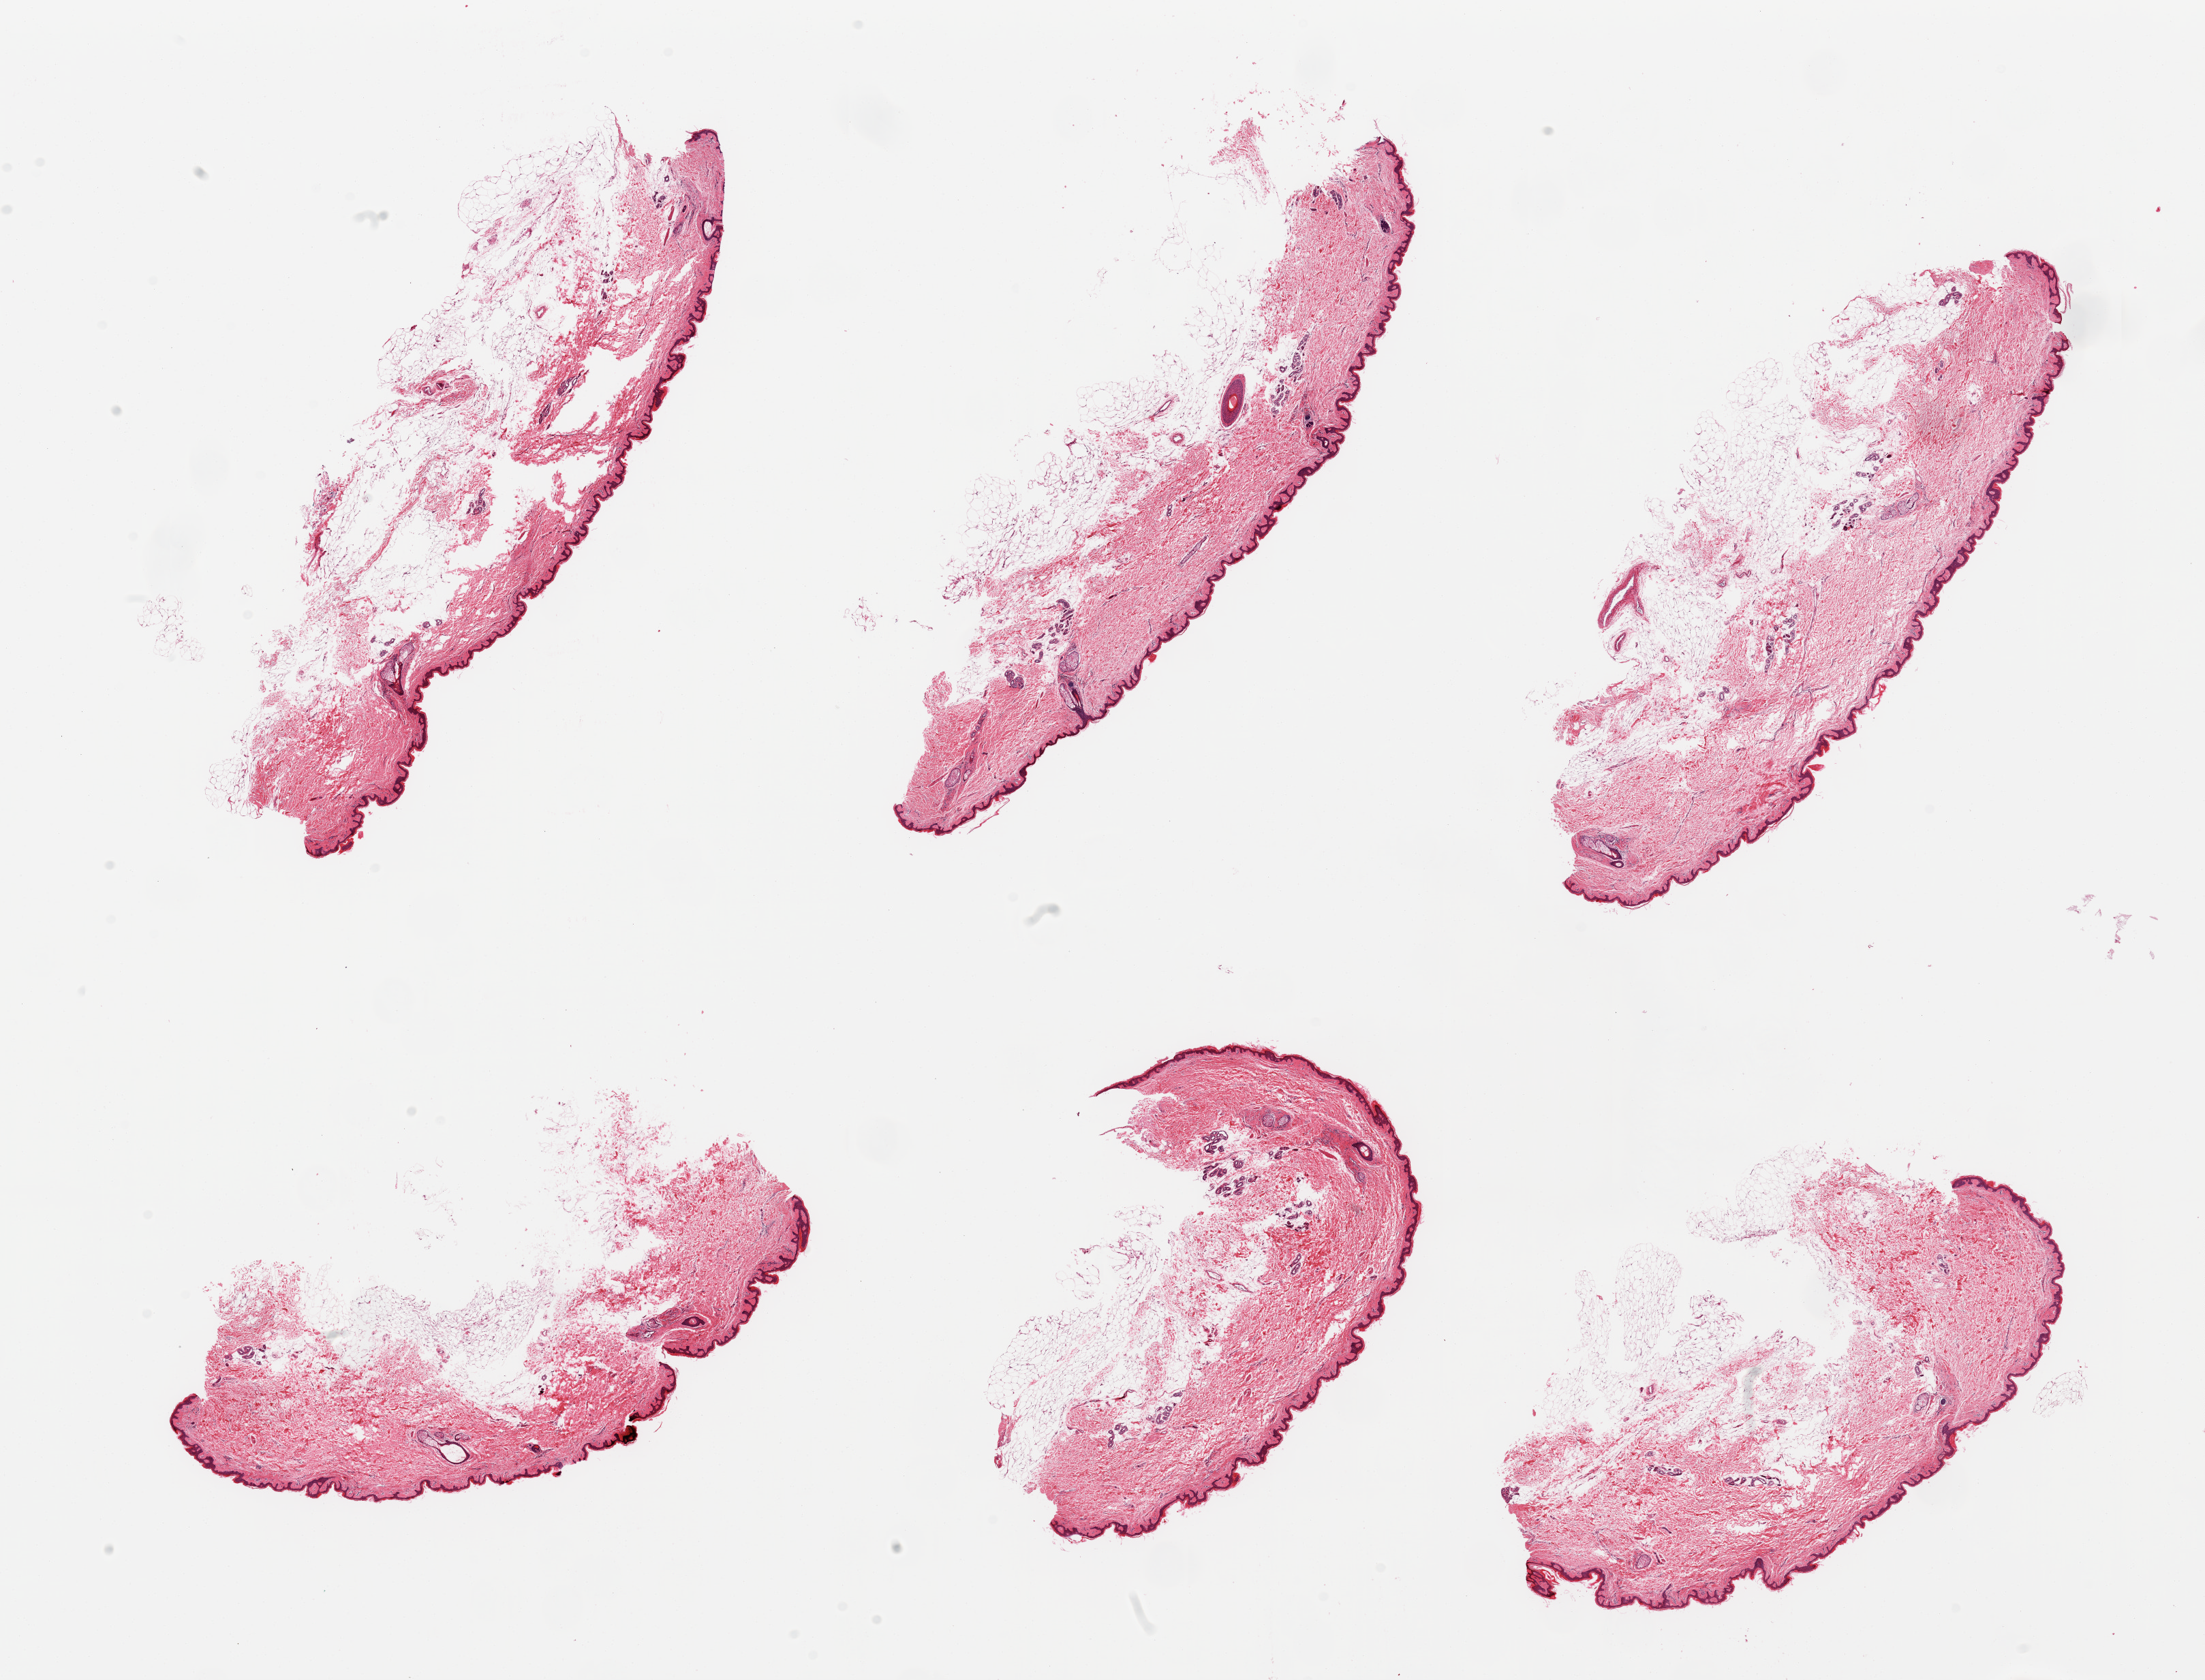
Whole-slide image, haematoxylin and eosin stain, whole scanned area (about 25.6 x 19.5 mm) shown as a low-resolution overview; PAXgene-fixed paraffin-embedded (PFPE) section; target tissue: skin of suprapubic region; donor tissue sample. Female donor.
Review note (as recorded): 6 pieces; excessive subcutaneous fat, up to 2mm thick plus thin fatty dermis.